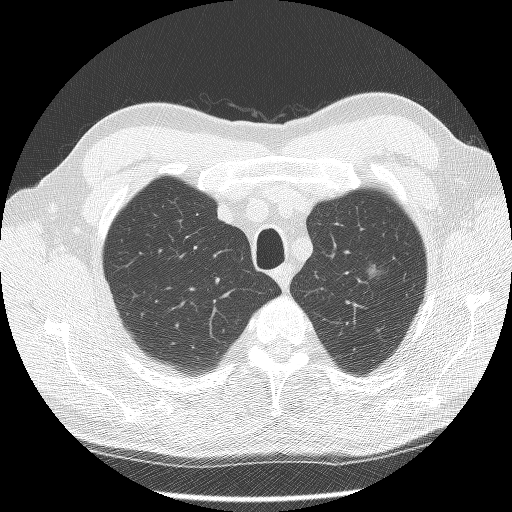
Axial slice from a low-dose chest CT screening exam, second screening round (one year after baseline), lung window (W 1500 / L -600 HU), lung (sharp) reconstruction kernel (BONE), slice 22 of 124 in the series, 512 × 512 image matrix. Male, age 60 years at enrolment. Former smoker at enrolment.
- Expert-annotated lung lesion, bounding box [x1, y1, x2, y2] px = [351, 254, 402, 297].
- The screening reader recorded 2 non-calcified nodules or masses ≥4 mm on this exam; which of them this box marks is not recorded.
- Official screen result: positive, no significant change: stable abnormalities potentially related to lung cancer, unchanged since the prior screening exam.
- Later outcome: lung cancer diagnosed 448 days after this screen (after the third annual screen) — bronchiolo-alveolar carcinoma, non-mucinous, left upper lobe, well differentiated (G1), stage IA (AJCC 6th edition), 16 mm at pathology.